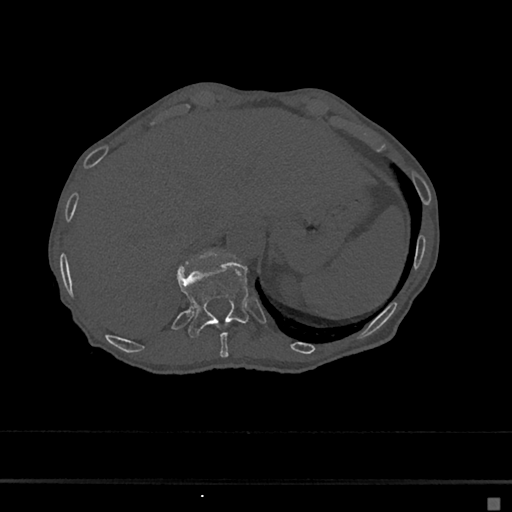
CT including the spine, one axial slice; slice 183 of 797 in the series (ordered by position); reconstruction kernel Br40s/3; 120 kVp; bone window (W 1800 / L 400 HU); 512 × 512 image matrix. Female patient, age 68 years. From the clinical record (not read from this slice): primary cancer: renal.
Outlined on this slice (semi-automatic segmentation, software-assisted and operator-edited):
- T10 vertebra: bounding box <216,324,228,357> (left, top, right, bottom; pixels)
- T11 vertebra: <177,261,250,338>
- T12 vertebra: <201,251,210,259>